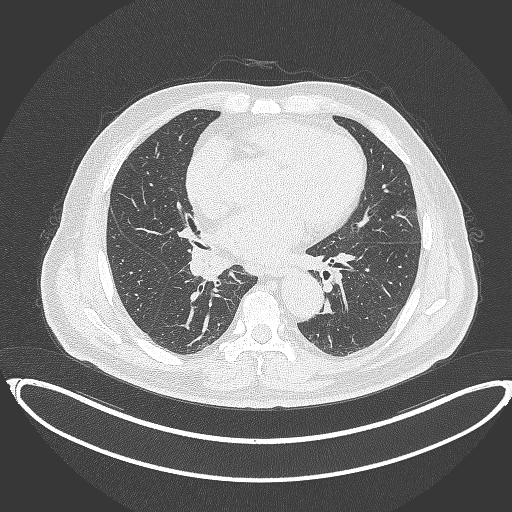
Chest CT, one axial slice. Position 195 of 387 along the scan axis. Reconstruction kernel B70f. 120 kVp. Lung window (W 1500 / L -600 HU). 512 × 512 image matrix, field of view 448 × 448 mm. Patient: male, 61 years. From the clinical record (not read from this slice): clinical TNM (as recorded): T1b N1 M0.
Structures marked on this image (rectangle marked by the reading radiologist):
- lung tumour (recorded histology: squamous cell carcinoma): bounding box (x1, y1, x2, y2) in pixels: (185, 245, 235, 287)